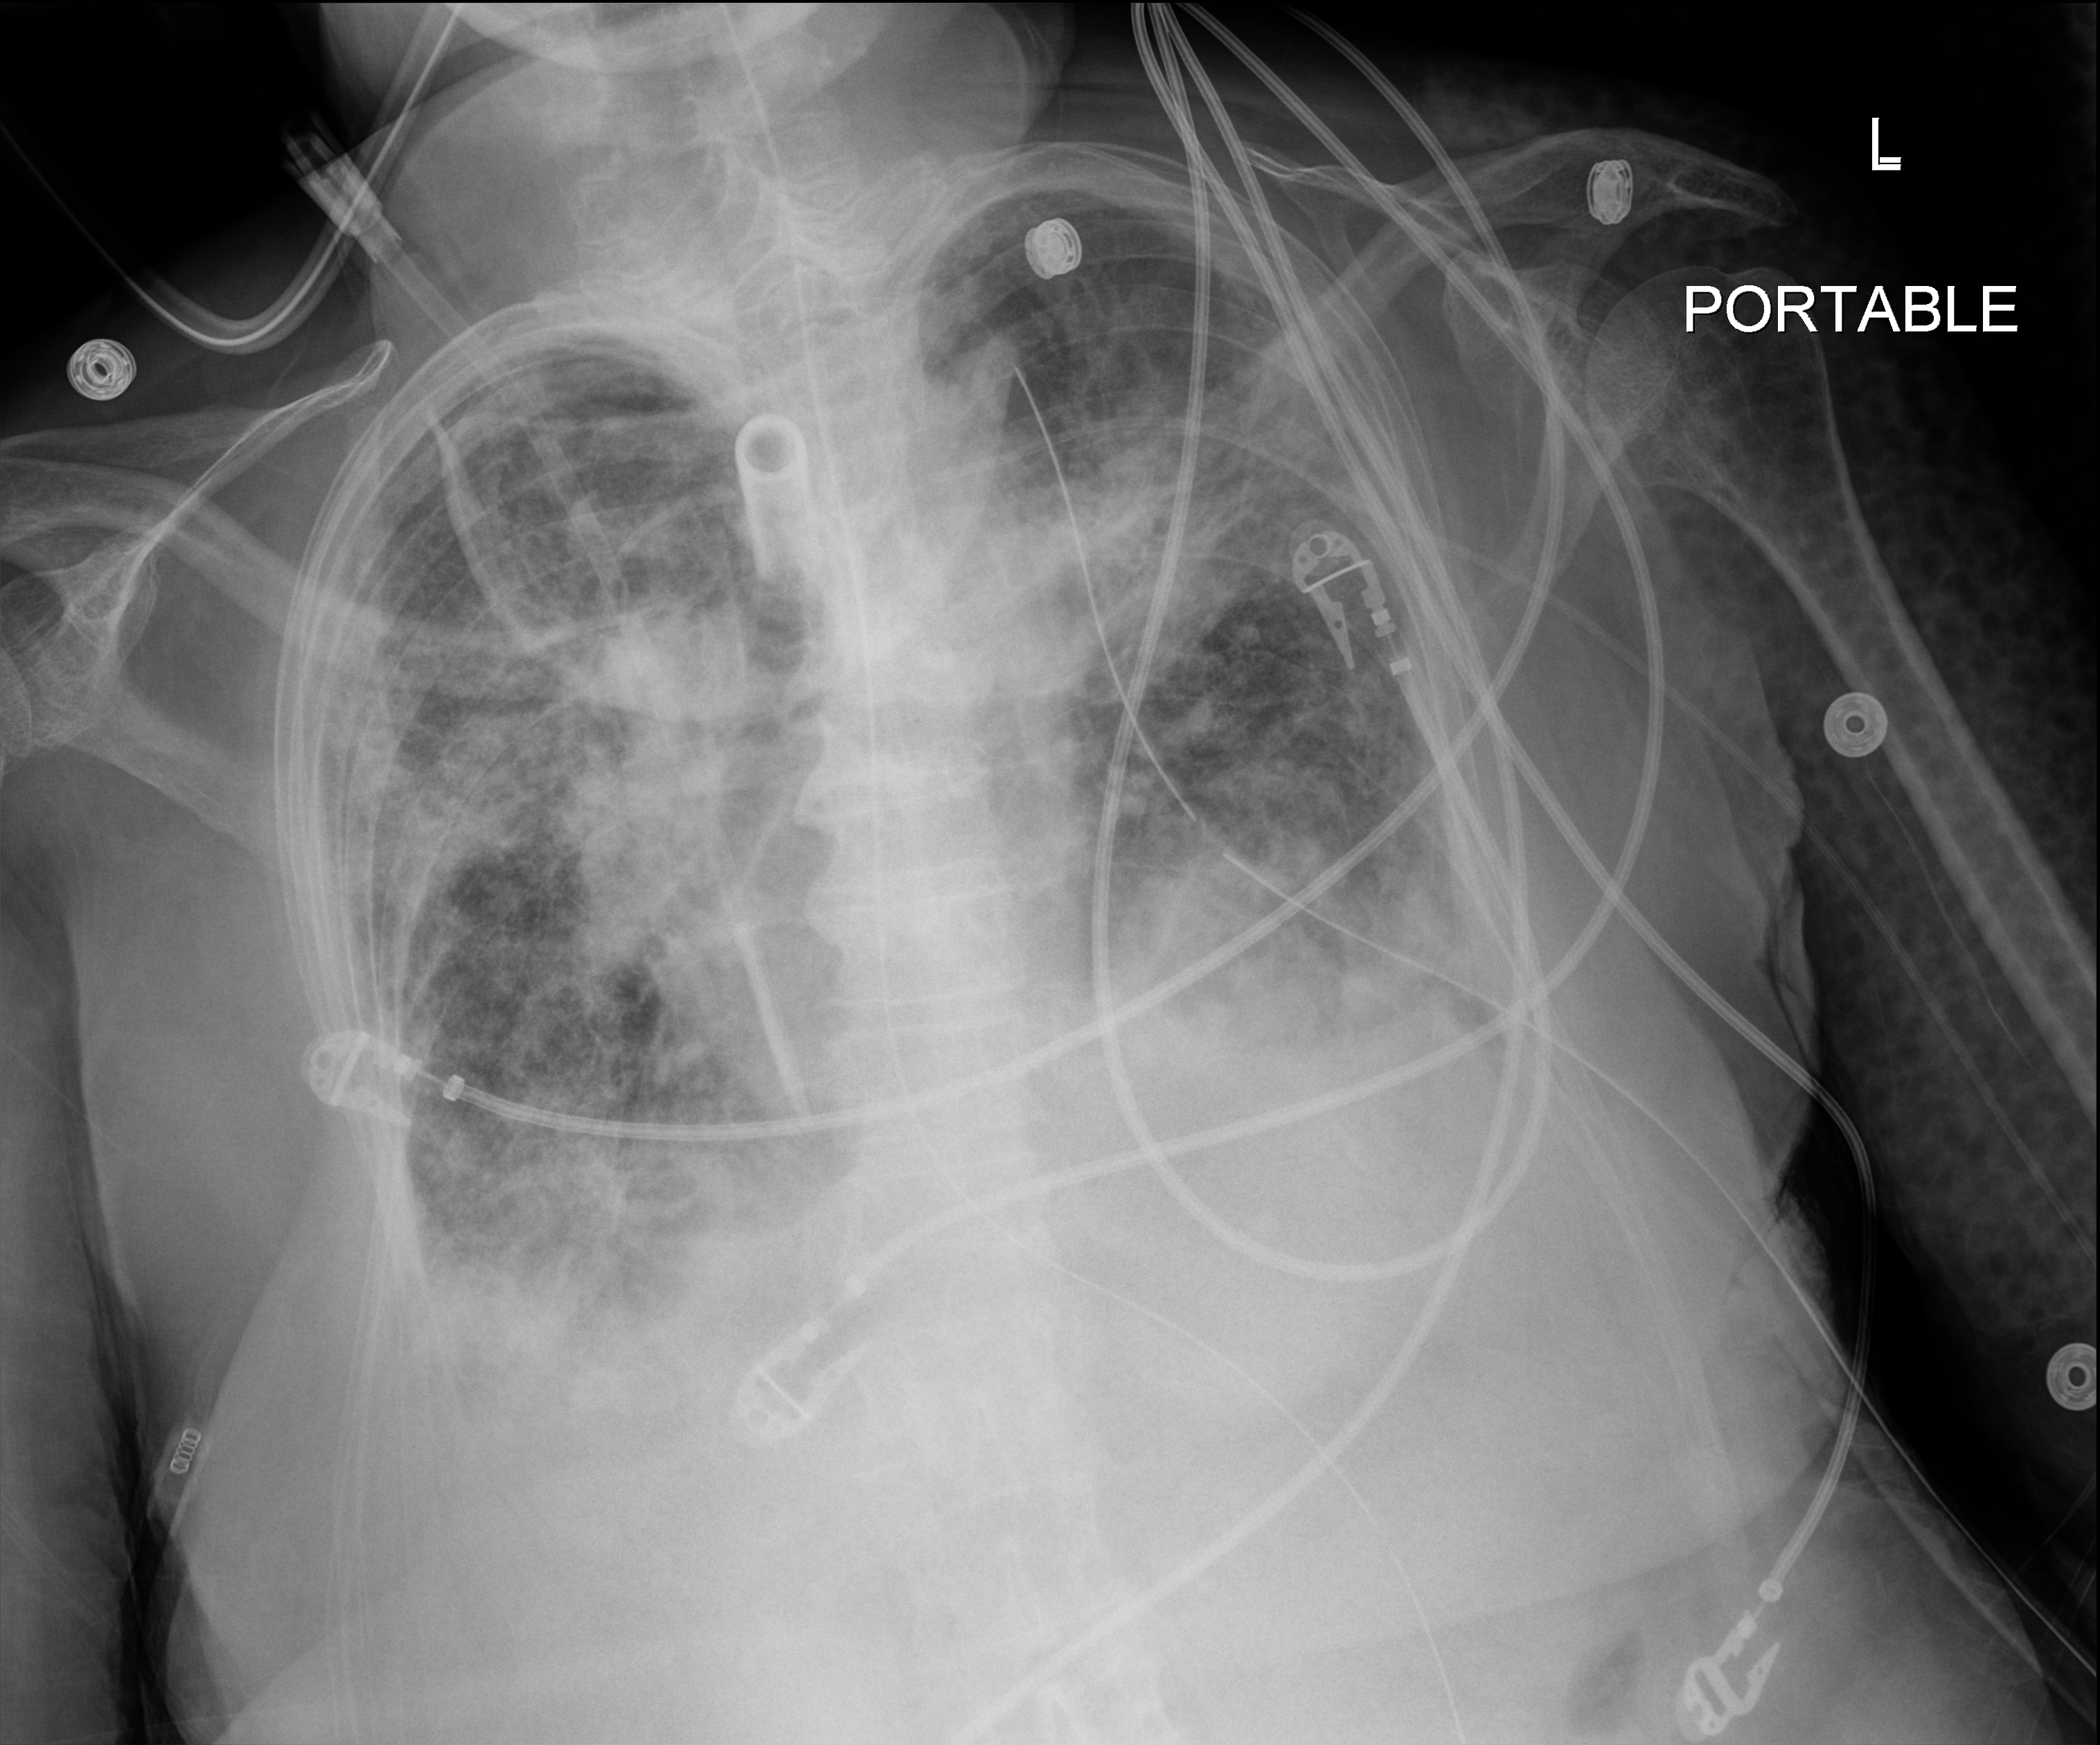
Chest X-ray; anteroposterior (AP) projection. Patient hospitalised with COVID-19; female, aged 75–90 years.
From the hospital-stay record, not from the radiograph (when in the stay this image was taken is not recorded):
- COPD (admission record): no